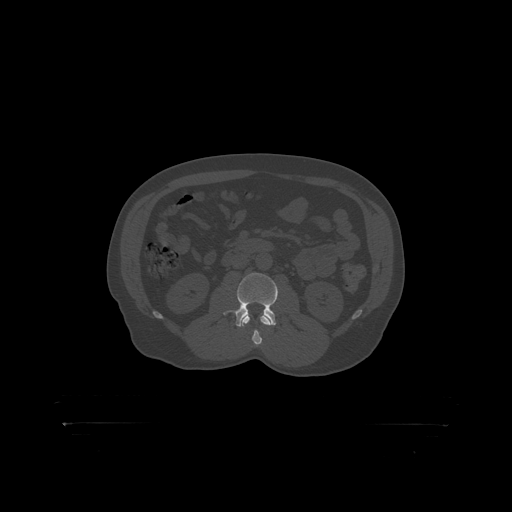
CT including the spine, one axial slice. Position 278 of 399 along the scan axis. 120 kVp. Bone window (W 1800 / L 400 HU). 512 × 512 image matrix. Male patient, age 46 years. Case-level facts recorded for this patient, not image findings: primary cancer: skin.
Outlined on this slice (semi-automatic segmentation, software-assisted and operator-edited):
- L2 vertebra: box from (x=244, y=315) to (x=266, y=319) px
- L3 vertebra: (x=228, y=273)–(x=278, y=319)